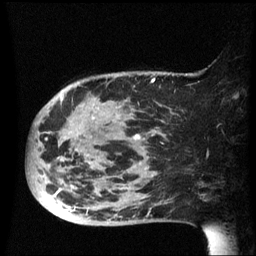
Breast MRI (dynamic contrast-enhanced), one sagittal slice; position 19 of 60 along the scan axis; dynamic contrast-enhanced series, image 2 of 3 at this slice position (ordered by acquisition); 1.5 T; TE 4.2 ms, TR 8.4 ms; 2.5 mm slice thickness; 256 × 256 image matrix, field of view 220 × 220 mm. Female patient, age 49 years.
Outlined on this slice (semi-automatic segmentation, software-assisted and operator-edited):
- analysis volume of interest (the breast-tissue region the enhancement analysis was run in; not a lesion): bounding box [x1, y1, x2, y2] px = [28, 72, 185, 227]
- tumour enhancement mask (voxels above the 70 % enhancement threshold inside the analysis volume of interest): [62, 78, 156, 225]